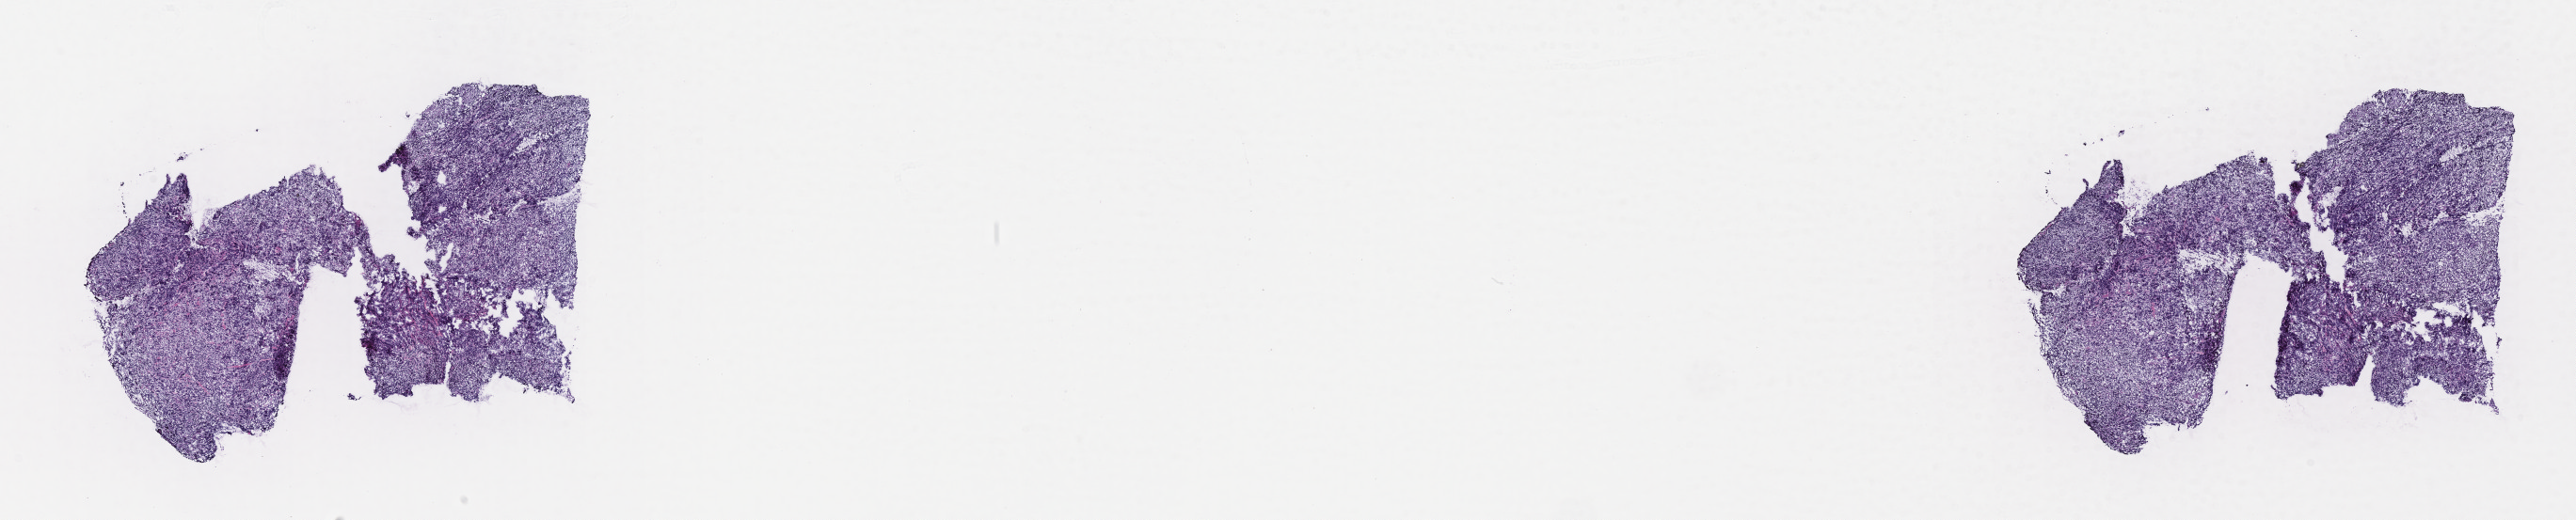
Whole-slide image, hematoxylin and eosin (H&E) stain — a low-resolution overview of the entire scanned area, about 22.1 x 4.5 mm; frozen section; primary tumor; anatomic site: abdomen proper. Male, age 4 years at initial diagnosis. Composition of this section per pathologist review: tumor cells 90%, tumor nuclei 90%, stromal cells 5%, necrosis 5%, normal cells 0%. Inflammatory infiltration, as recorded: lymphocyte infiltration 75%, monocyte infiltration 20%, neutrophil infiltration 5%.
* Ann Arbor stage (patient): Stage II
* histologic diagnosis: Burkitt lymphoma, NOS